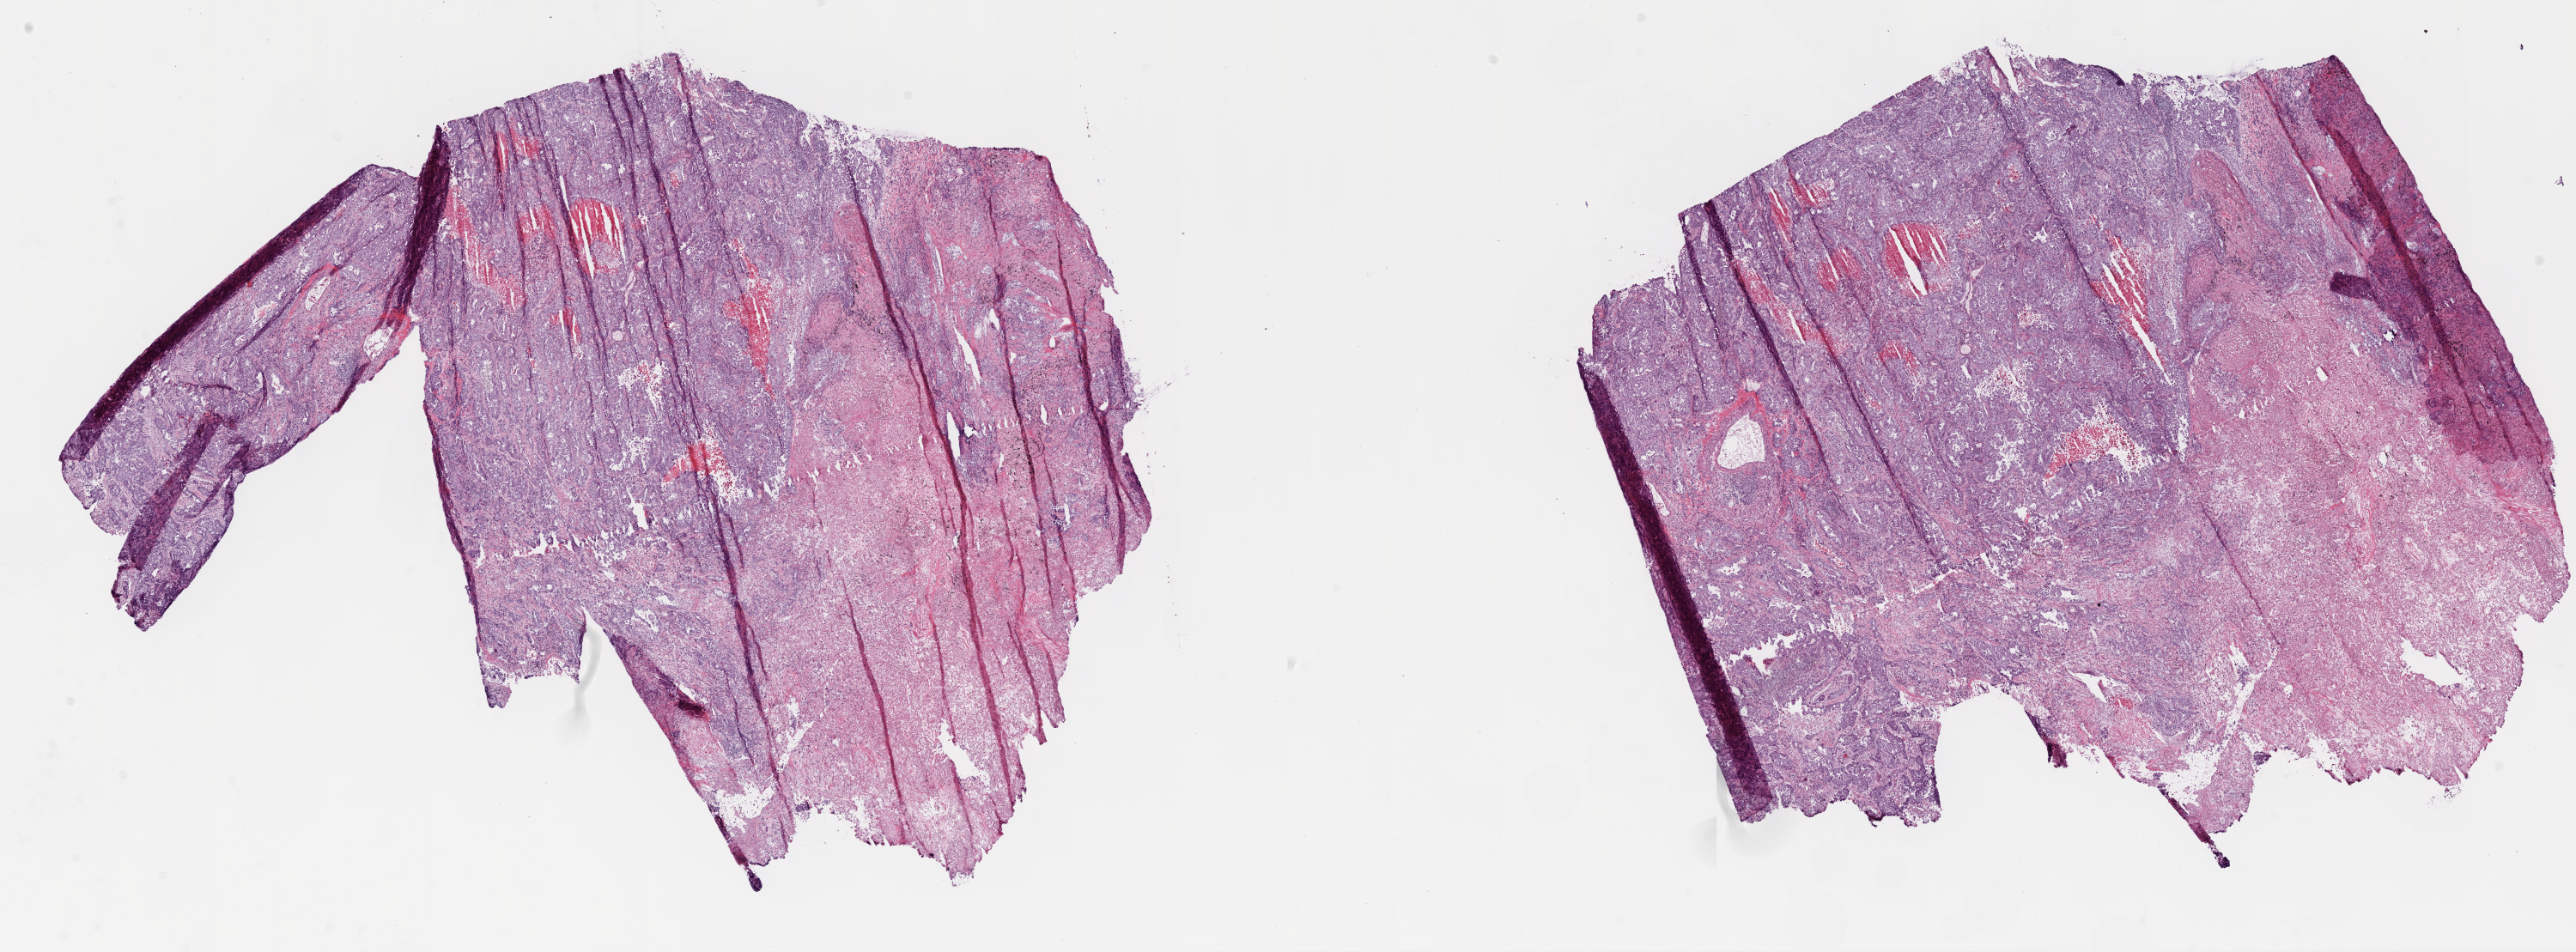
Whole-slide histology image, H&E, whole scanned area (about 24.1 x 8.9 mm, slide scanned at 20x) shown as a low-resolution overview. Frozen section from the top of the tissue portion. Sample: primary tumour, lung. Female patient; age at initial diagnosis 77 years. Slide review estimates, as recorded: tumour nuclei 75%, normal cells 0%, stromal cells 40%, necrosis 18%.
* laterality: left
* AJCC pathologic stage: IA
* diagnosis: Adenocarcinoma, NOS (upper lobe, lung)